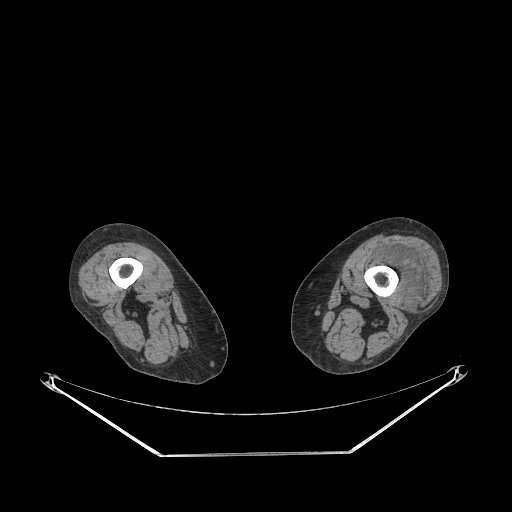
CT of an extremity soft-tissue mass (from a PET/CT study), one axial slice; slice 198 of 267 in the series (ordered by position); soft-tissue window (W 400 / L 40 HU); 512 × 512 image matrix, field of view 500 × 500 mm. Female patient. Case-level facts recorded for this patient, not image findings: histological type: undifferentiated – high grade; grade: high; site of the primary tumour: left thigh.
Structures marked on this image (expert contour drawn on MRI and transferred to this co-registered scan by the dataset authors):
- gross tumour volume including surrounding oedema: bounding box <372,246,430,302> (left, top, right, bottom; pixels)